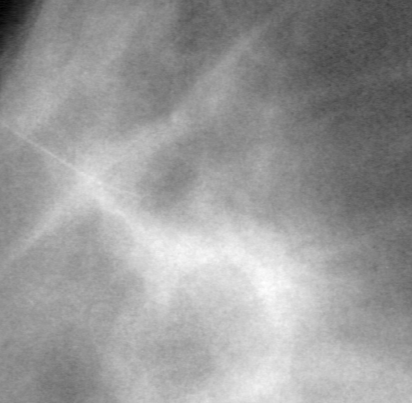
Cropped region of a digitized screen-film mammogram centred on a radiologist-marked abnormality, left breast, MLO view, BI-RADS breast density category 4 (scale 1–4).
- Marked abnormality: mass, shape irregular, margins ill defined; BI-RADS assessment category 4; pathology (as recorded): benign.